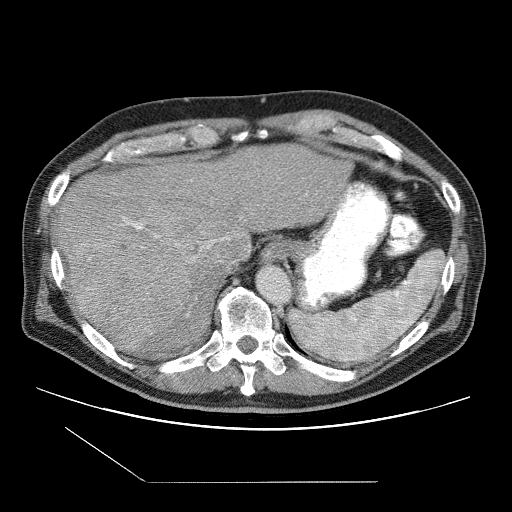
Contrast-enhanced abdominal CT (liver protocol), one axial slice. Slice 79 of 109 in the series (ordered by position). One of 2 acquisitions stored at this slice position. Soft-tissue window (W 400 / L 40 HU). 2.5 mm slice thickness. 512 × 512 image matrix. From the clinical record (not read from this slice): diagnosis: hepatocellular carcinoma (patient treated with transarterial chemoembolisation; whether this scan precedes or follows treatment is not stated here); TNM stage (as recorded): Stage-IIIB; Child-Pugh class: A; tumour differentiation: well differentiated; tumour nodularity: multinodular.
Outlined on this slice (semi-automatic segmentation, software-assisted and operator-edited):
- liver parenchyma outside the tumour (the mass and vessels are separate outlines, so this box may not span the whole liver): bounding box (x1, y1, x2, y2) in pixels: (54, 144, 350, 350)
- mass: (69, 232, 192, 348)
- liver vessels: (123, 218, 229, 249)